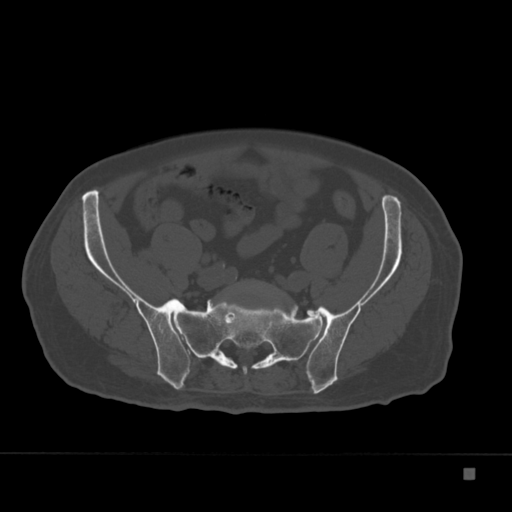
CT including the spine, one axial slice. Slice 5 of 332 in the series (ordered by position). Reconstruction kernel Br40s. 120 kVp. Bone window (W 1800 / L 400 HU). 1.5 mm slice thickness. 512 × 512 image matrix, field of view 389 × 389 mm. Patient: male, 72 years. Case-level facts recorded for this patient, not image findings: primary cancer: skeletal.
Annotated regions visible in this slice (semi-automatic segmentation, software-assisted and operator-edited):
- L5 vertebra: bounding box (x1, y1, x2, y2) in pixels: (247, 283, 268, 308)